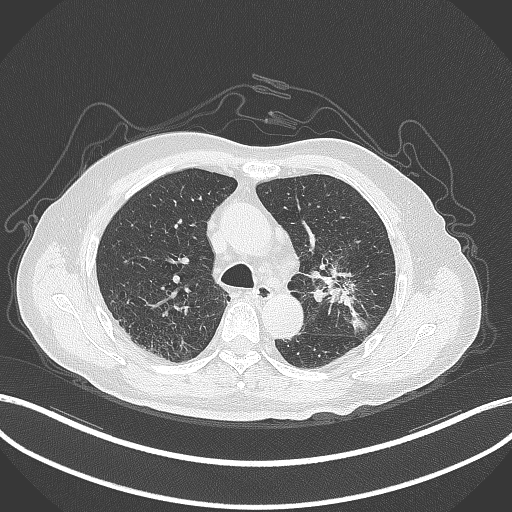
Chest CT, one axial slice; slice 192 of 331 in the series (ordered by position); reconstruction kernel B70f; 120 kVp; lung window (W 1500 / L -600 HU); 1 mm slice thickness; 512 × 512 image matrix. Male patient, age 79 years. Case-level facts recorded for this patient, not image findings: clinical TNM (as recorded): T2a N1 M1; histopathological grade: G3.
Annotated regions visible in this slice (rectangle marked by the reading radiologist):
- lung tumour (recorded histology: adenocarcinoma): bounding box (x1, y1, x2, y2) in pixels: (320, 272, 376, 339)